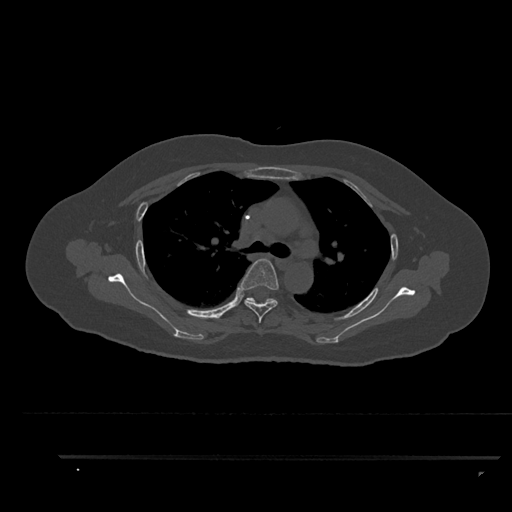
CT including the spine, one axial slice. Slice 634 of 797 in the series (ordered by position). Reconstruction kernel Br40s/3. 120 kVp. Bone window (W 1800 / L 400 HU). 0.5 mm slice thickness. 512 × 512 image matrix, field of view 408 × 408 mm. Female patient, age 44 years. Case-level facts recorded for this patient, not image findings: primary cancer: renal.
Outlined on this slice (semi-automatically segmented with operator editing):
- T4 vertebra: bounding box <241,259,279,323> (left, top, right, bottom; pixels)
- T5 vertebra: <244,297,269,302>